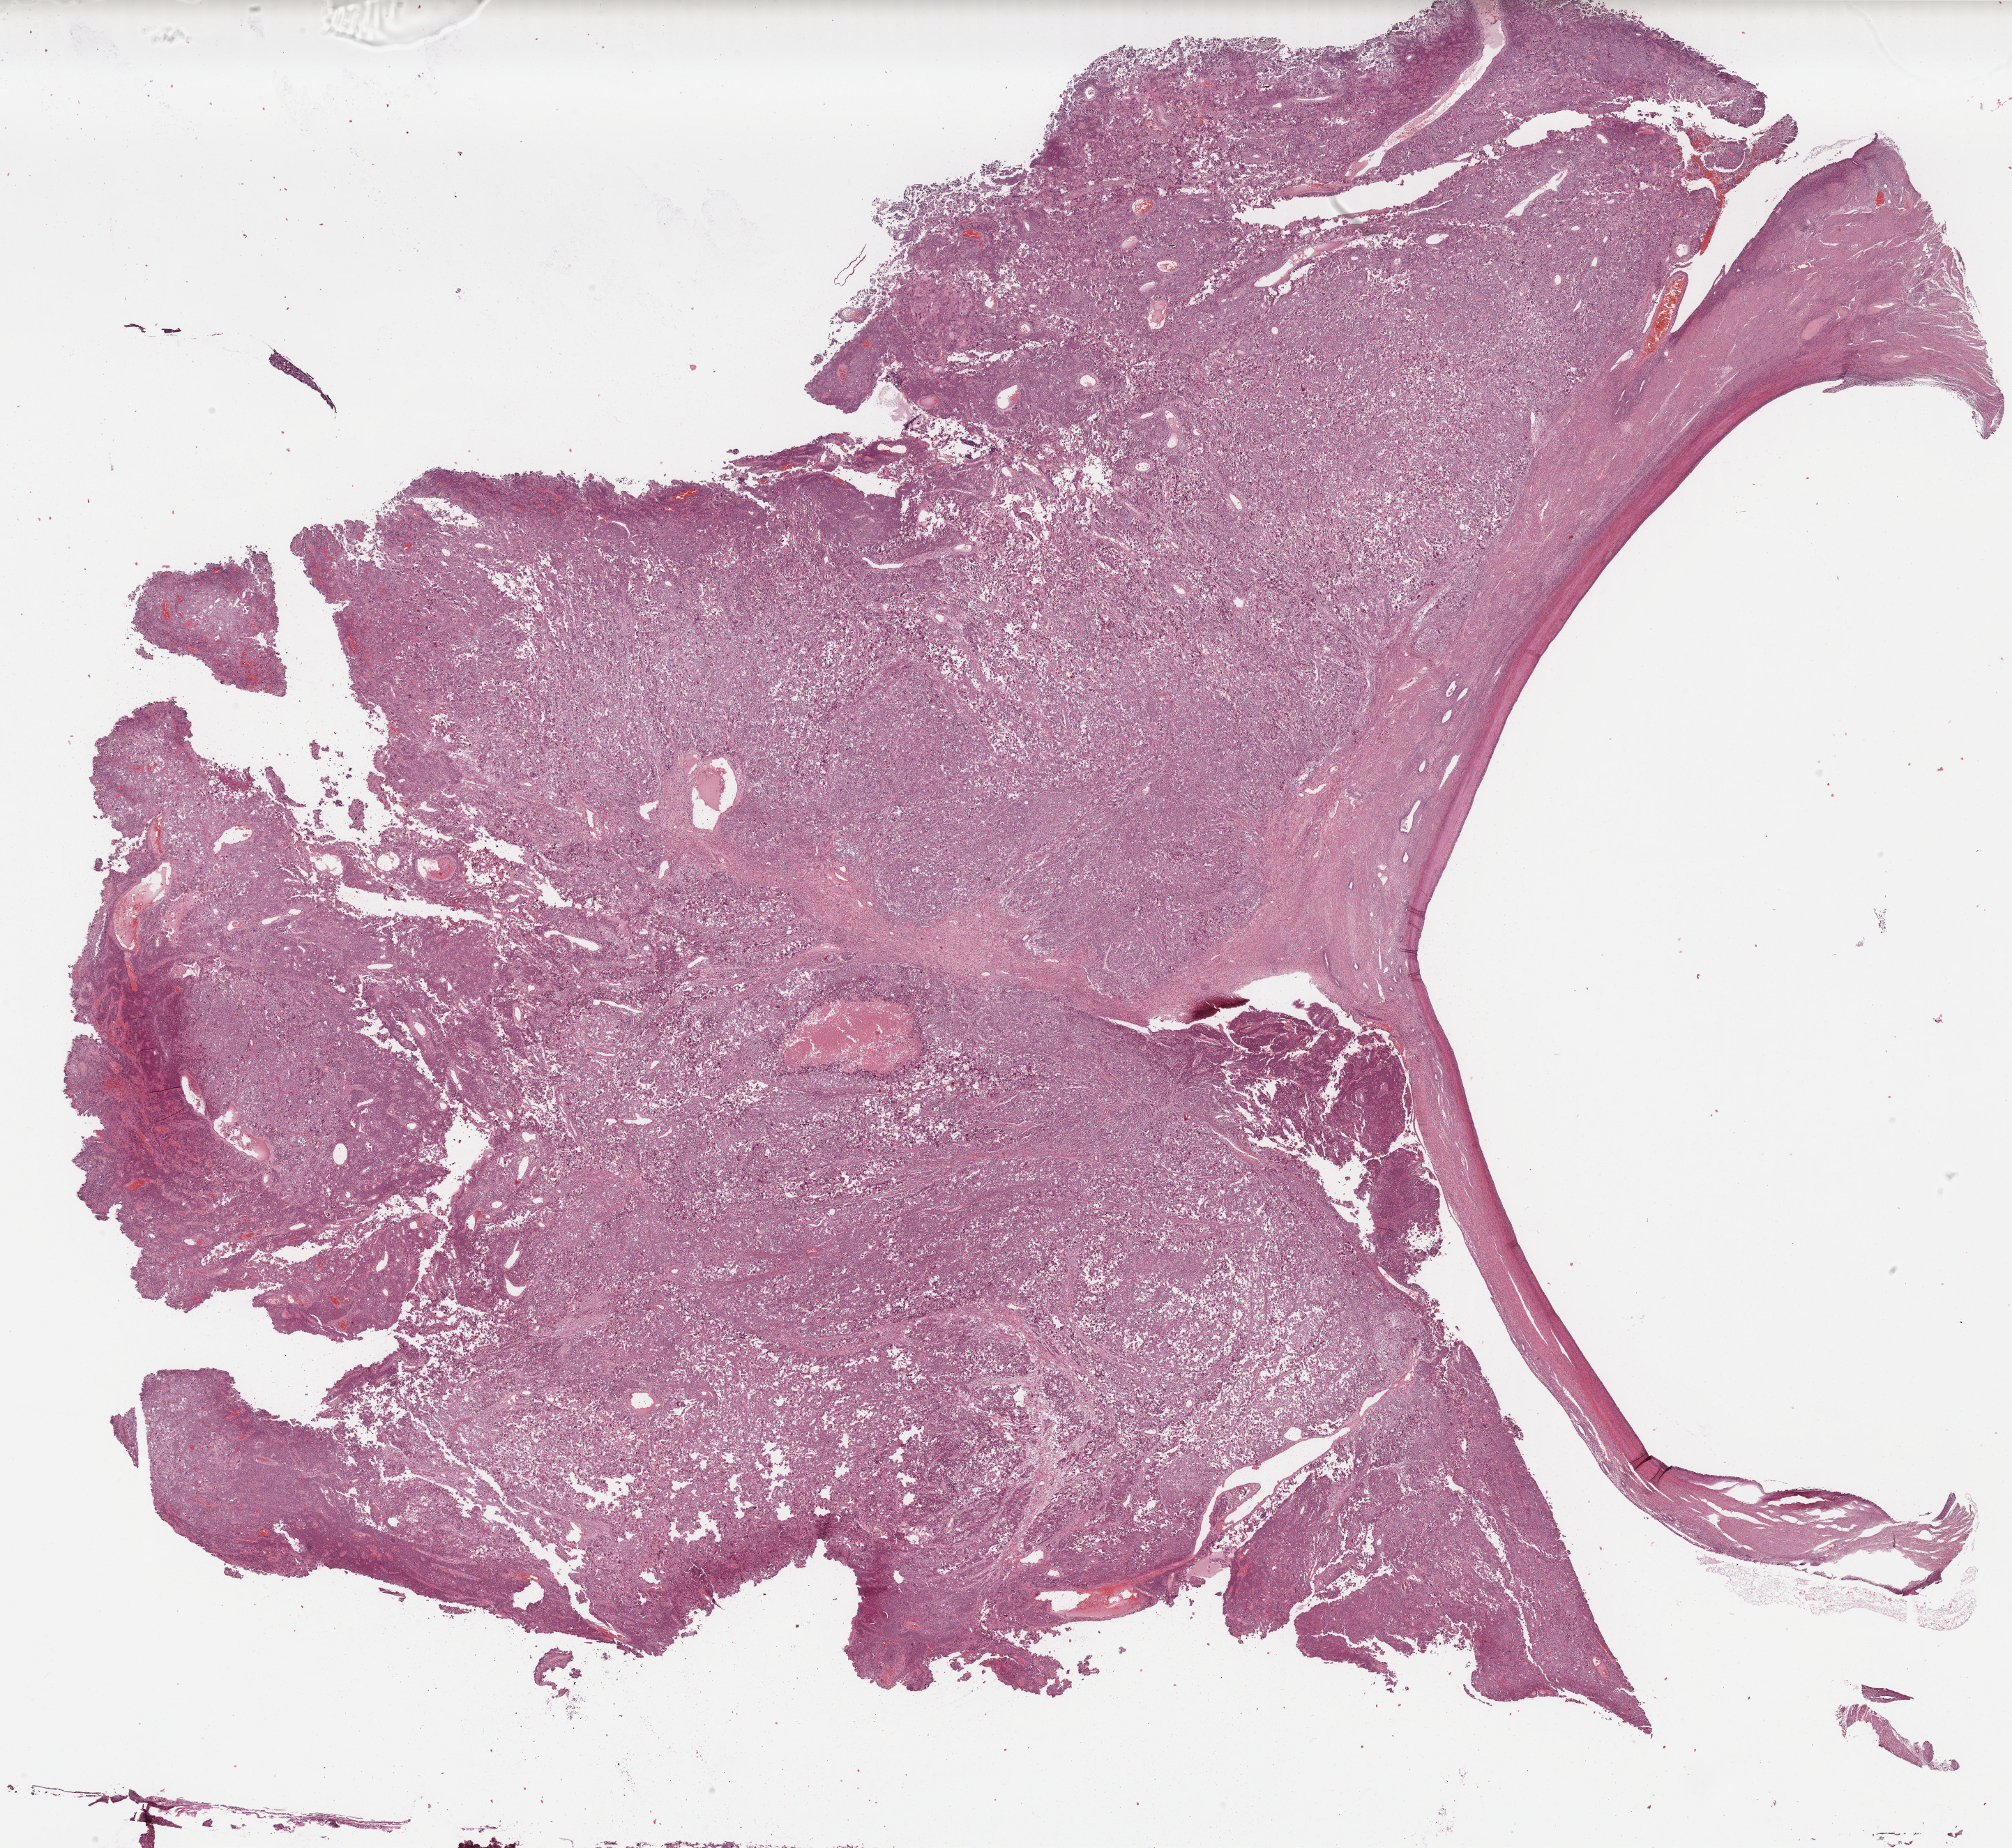
Whole-slide histology image, H&E-stained — a low-resolution overview of the entire scanned area, about 22.9 x 21.0 mm (from a 40x scan), formalin-fixed paraffin-embedded (FFPE) diagnostic section, uterus, primary tumour sample. Female, age 55 years at initial diagnosis. Histologic grade: G3 (poorly differentiated).
- lymph nodes positive (case pathology): 1 of 8 examined
- pathologic diagnosis: Endometrioid adenocarcinoma, NOS (endometrium)
- FIGO stage: IIIC